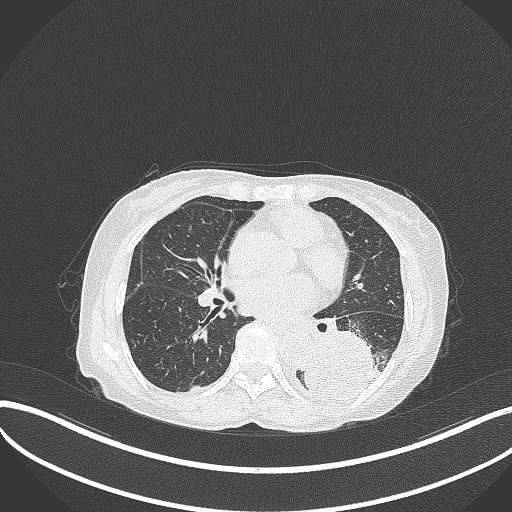
Chest CT, one axial slice; slice 146 of 370 in the series (ordered by position); 120 kVp; lung window (W 1500 / L -600 HU); 512 × 512 image matrix, field of view 400 × 400 mm. Female patient, age 78 years. From the clinical record (not read from this slice): clinical TNM (as recorded): T3 N0 M1.
Structures marked on this image (rectangle marked by the reading radiologist):
- lung tumour (recorded histology: squamous cell carcinoma): box from (x=297, y=325) to (x=388, y=401) px